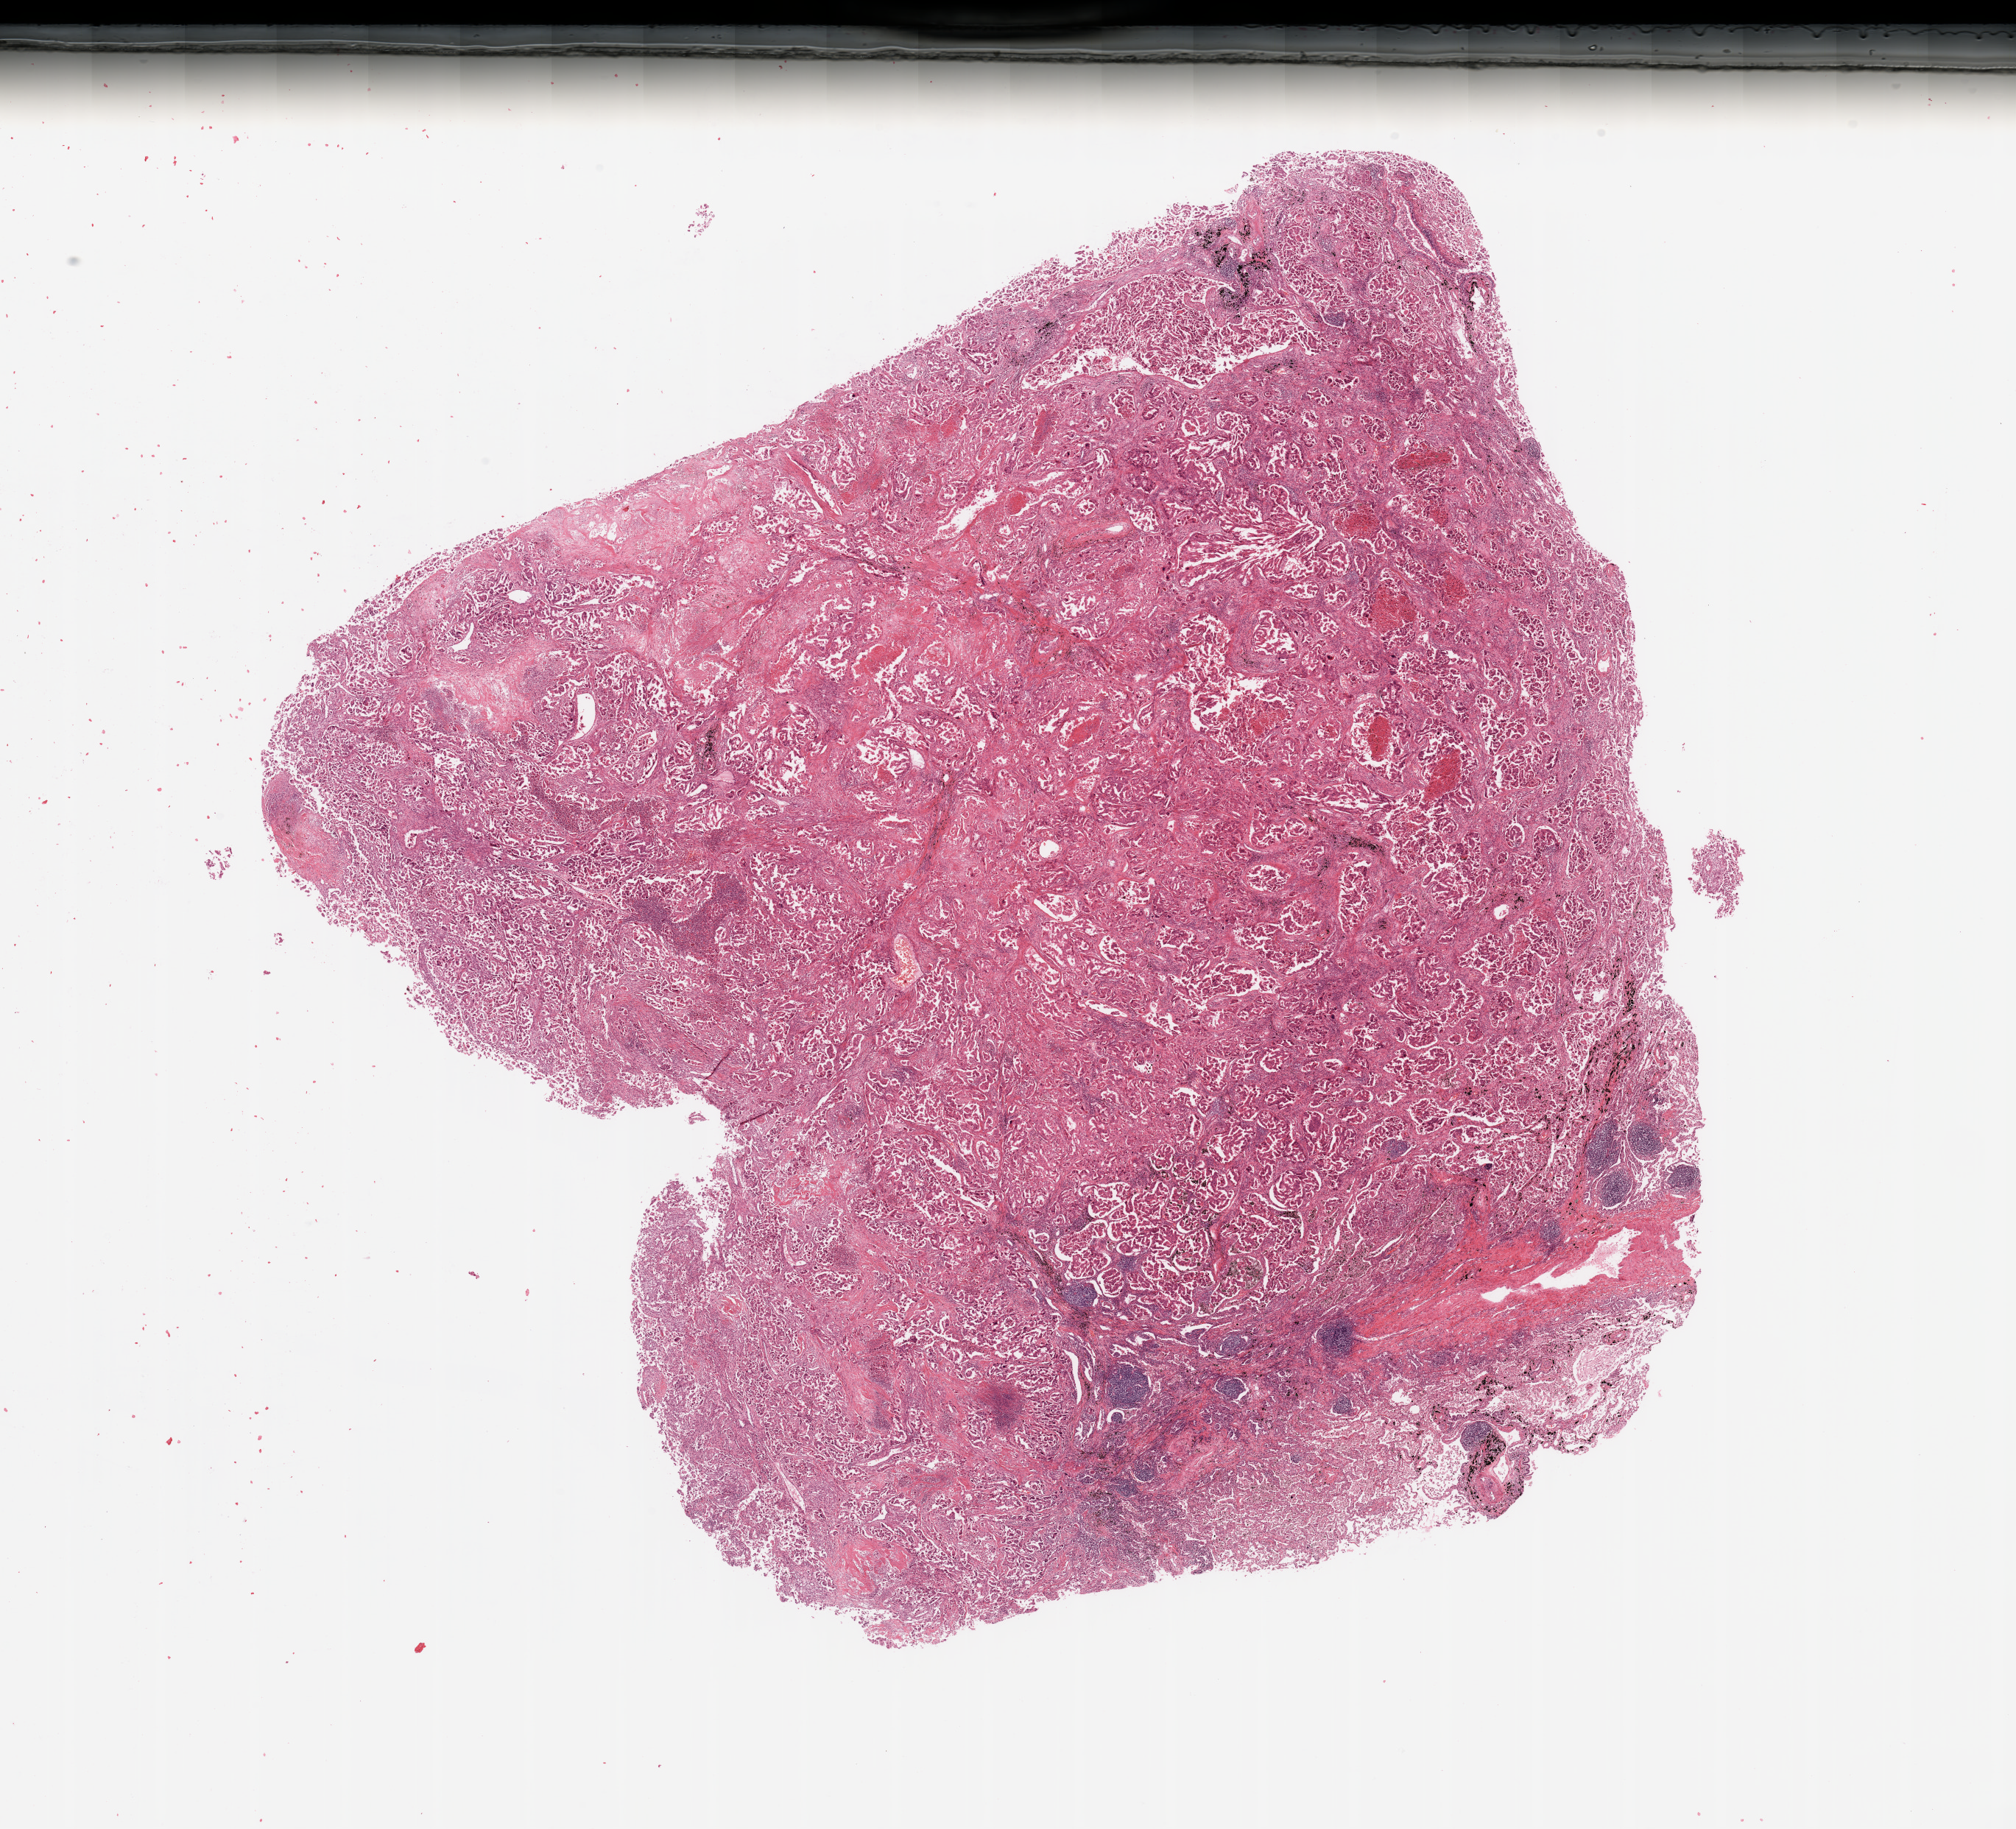
Digitized Hematoxylin and eosin (H&E) stained tissue section (whole slide), a low-resolution overview of the entire scanned area, about 21.7 x 19.6 mm, tumour tissue sample, sampled site: lung. 54-year-old male patient. Histologic grade: G2 (moderately differentiated). Composition of this section per pathologist review: tumour nuclei 70%, necrosis 15%.
Histologic diagnosis: Adenocarcinoma, NOS. AJCC pathologic stage: IB.